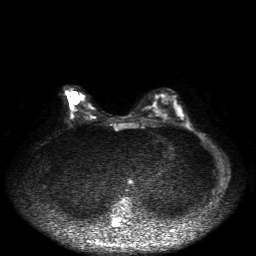
Breast MRI, one axial slice. Slice 18 of 50 in the series (ordered by position). Diffusion-weighted series; image 2 of 4 stored at this slice position (different b-values; order by instance number). 1.5 T. 4 mm slice thickness. 256 × 256 image matrix, field of view 360 × 360 mm. Female patient.
Outlined on this slice (manually delineated by an expert):
- tumour on diffusion-weighted imaging: bounding box (x1, y1, x2, y2) in pixels: (72, 96, 77, 104)